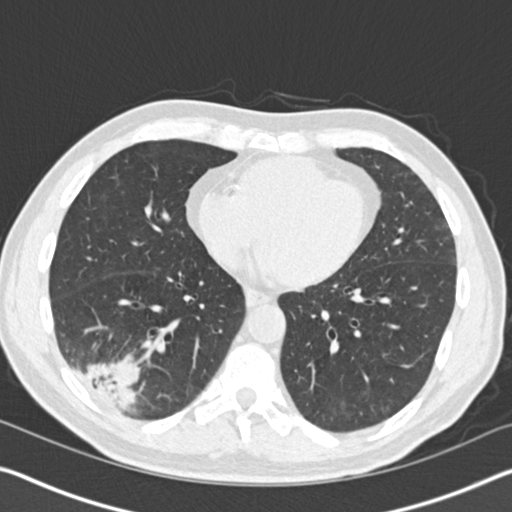
Low-dose screening chest CT, axial slice, baseline annual screen, lung window (W 1500 / L -600 HU), standard (soft-tissue) reconstruction kernel (B30f). Male participant, aged 61 years at enrolment. Current smoker at enrolment.
Expert reader's lesion annotation, bounding box <42,319,154,423> (left, top, right, bottom; pixels). Reader record for this screening exam (exam-level; its link to the box is not recorded): non-calcified nodule or mass ≥4 mm, right lower lobe, 52 × 36 mm, spiculated (stellate) margins, soft tissue attenuation. Lung cancer was diagnosed 392 days after this screen: bronchiolo-alveolar adenocarcinoma, NOS, right lower lobe, moderately differentiated (G2), stage IIIB (AJCC 6th edition), 90 mm at pathology.